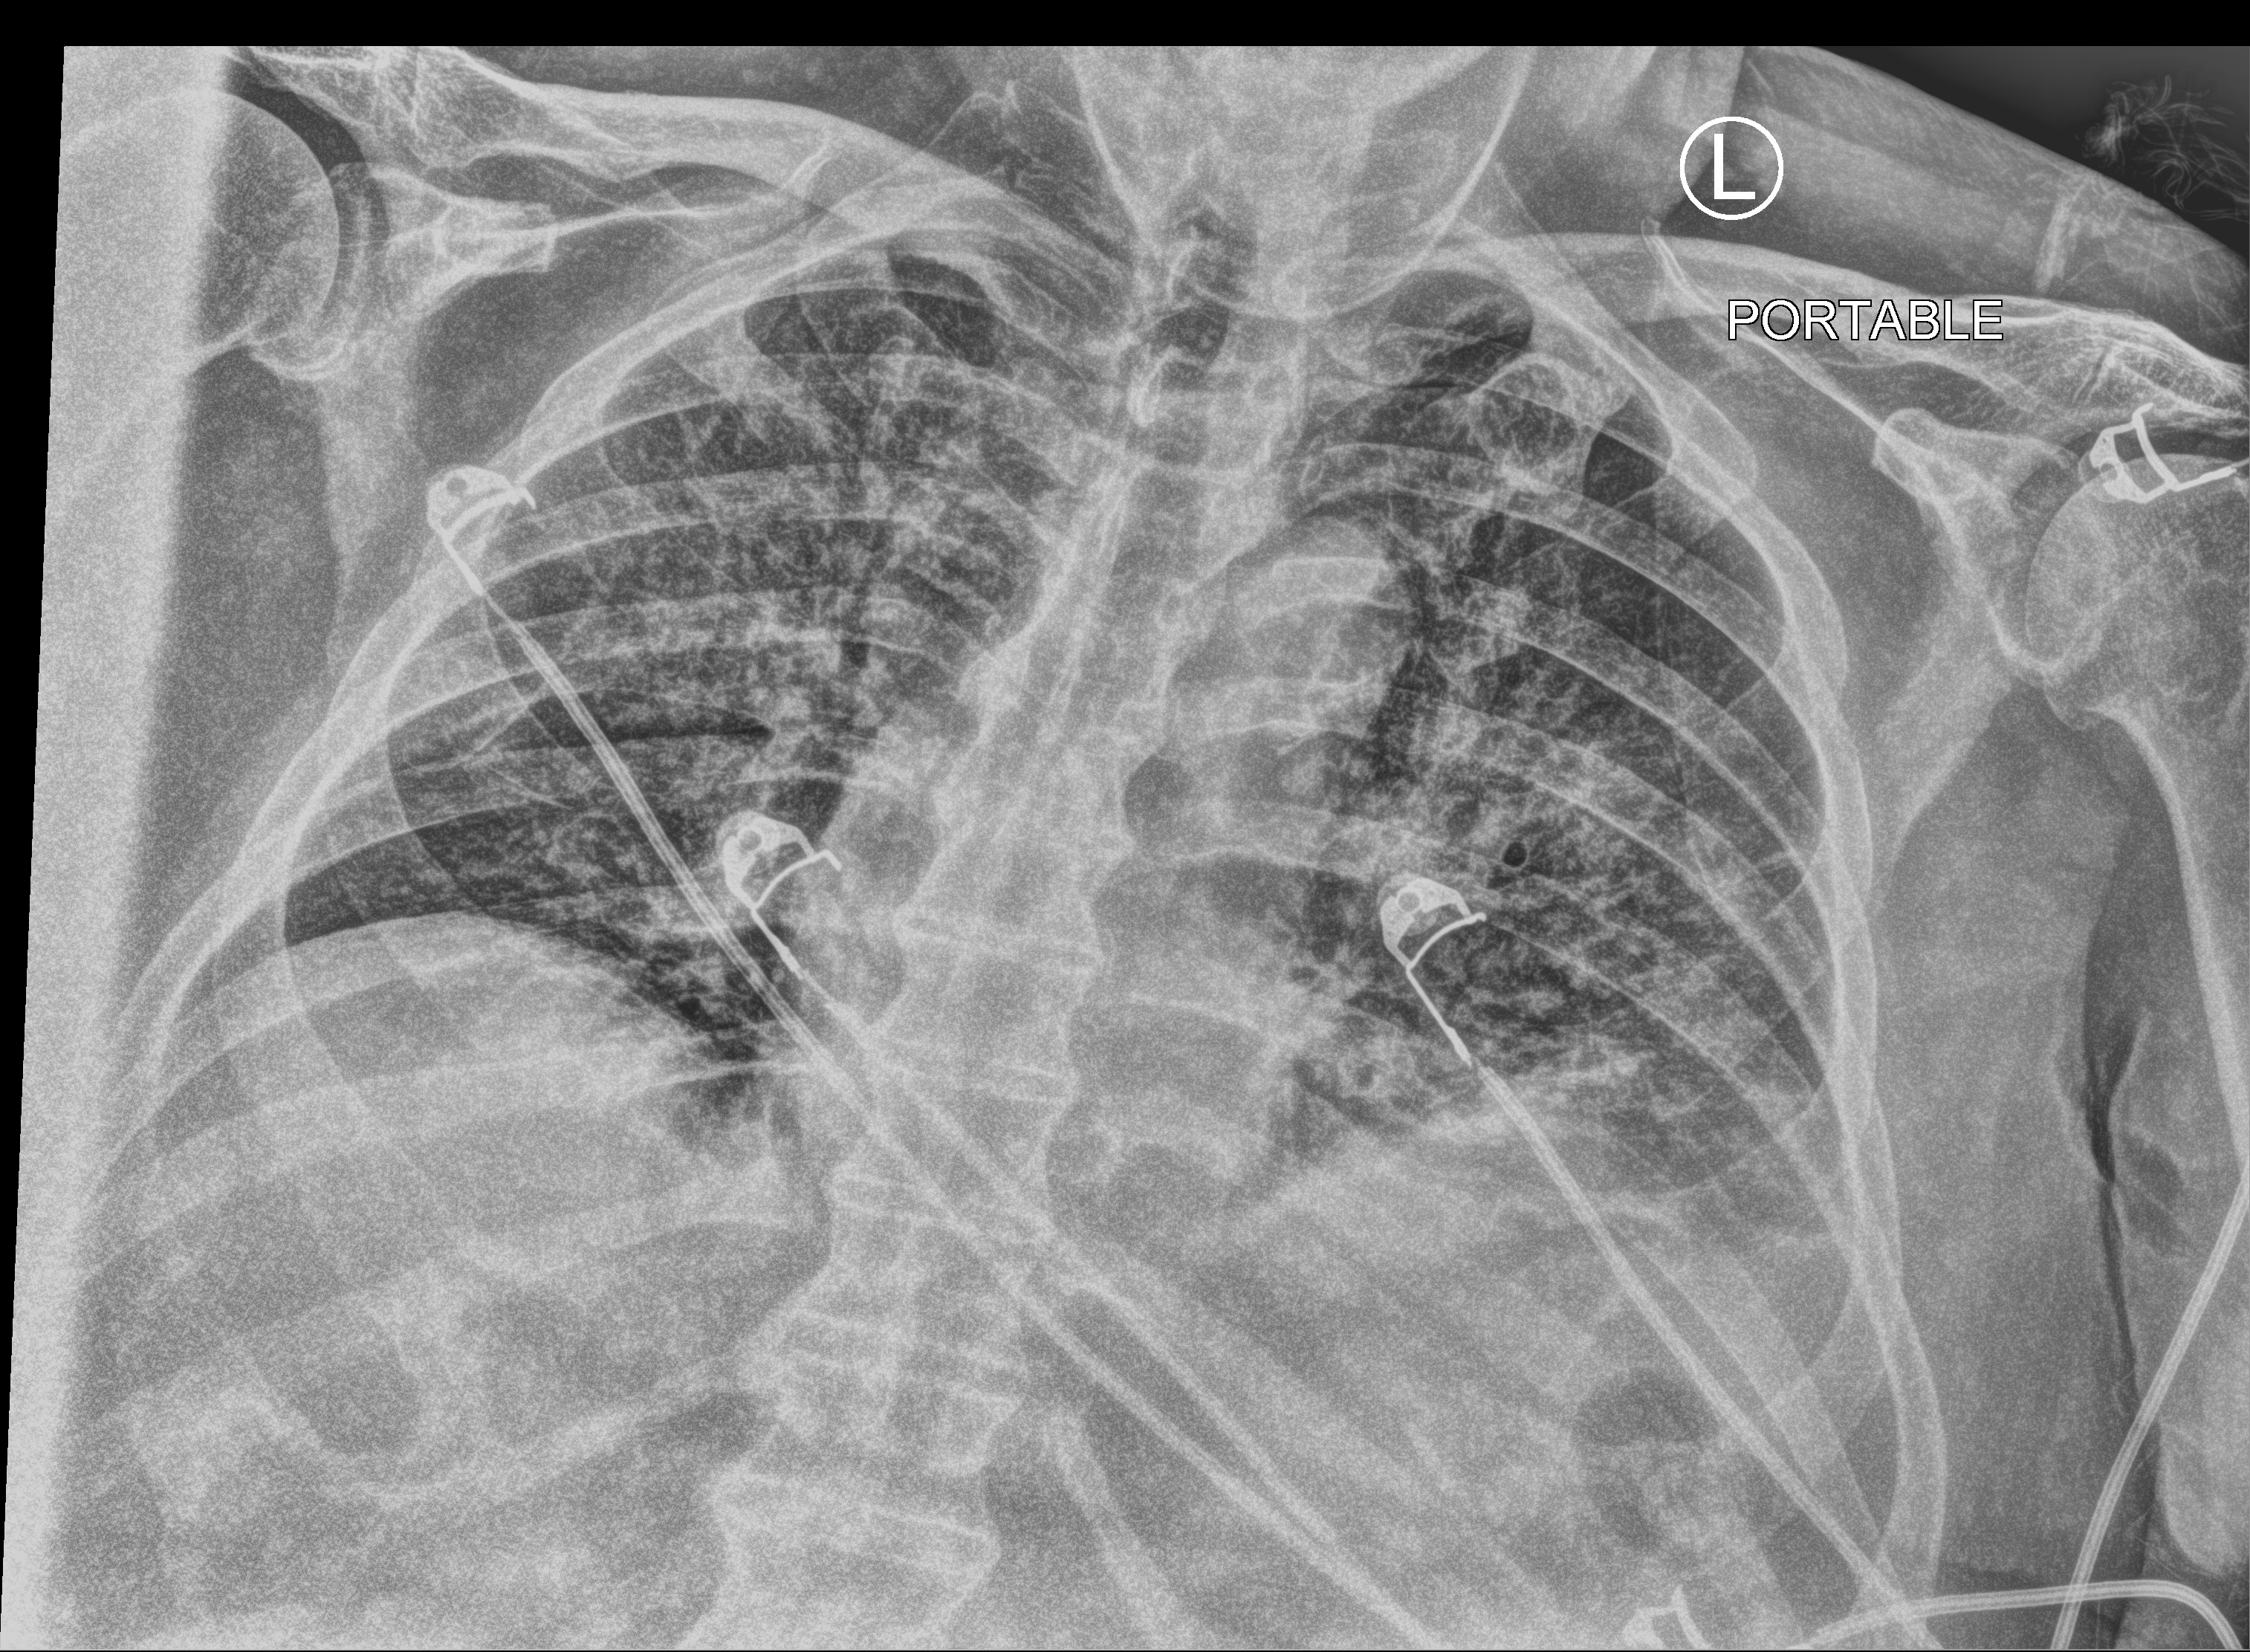
Chest X-ray (portable), anteroposterior (AP) projection. Patient hospitalised with COVID-19; male, aged 75–90 years.
Admission-level facts for this patient (not findings on this image; timing relative to this image not recorded): admitted to intensive care during this hospital stay: no; mechanically ventilated during this hospital stay: no.